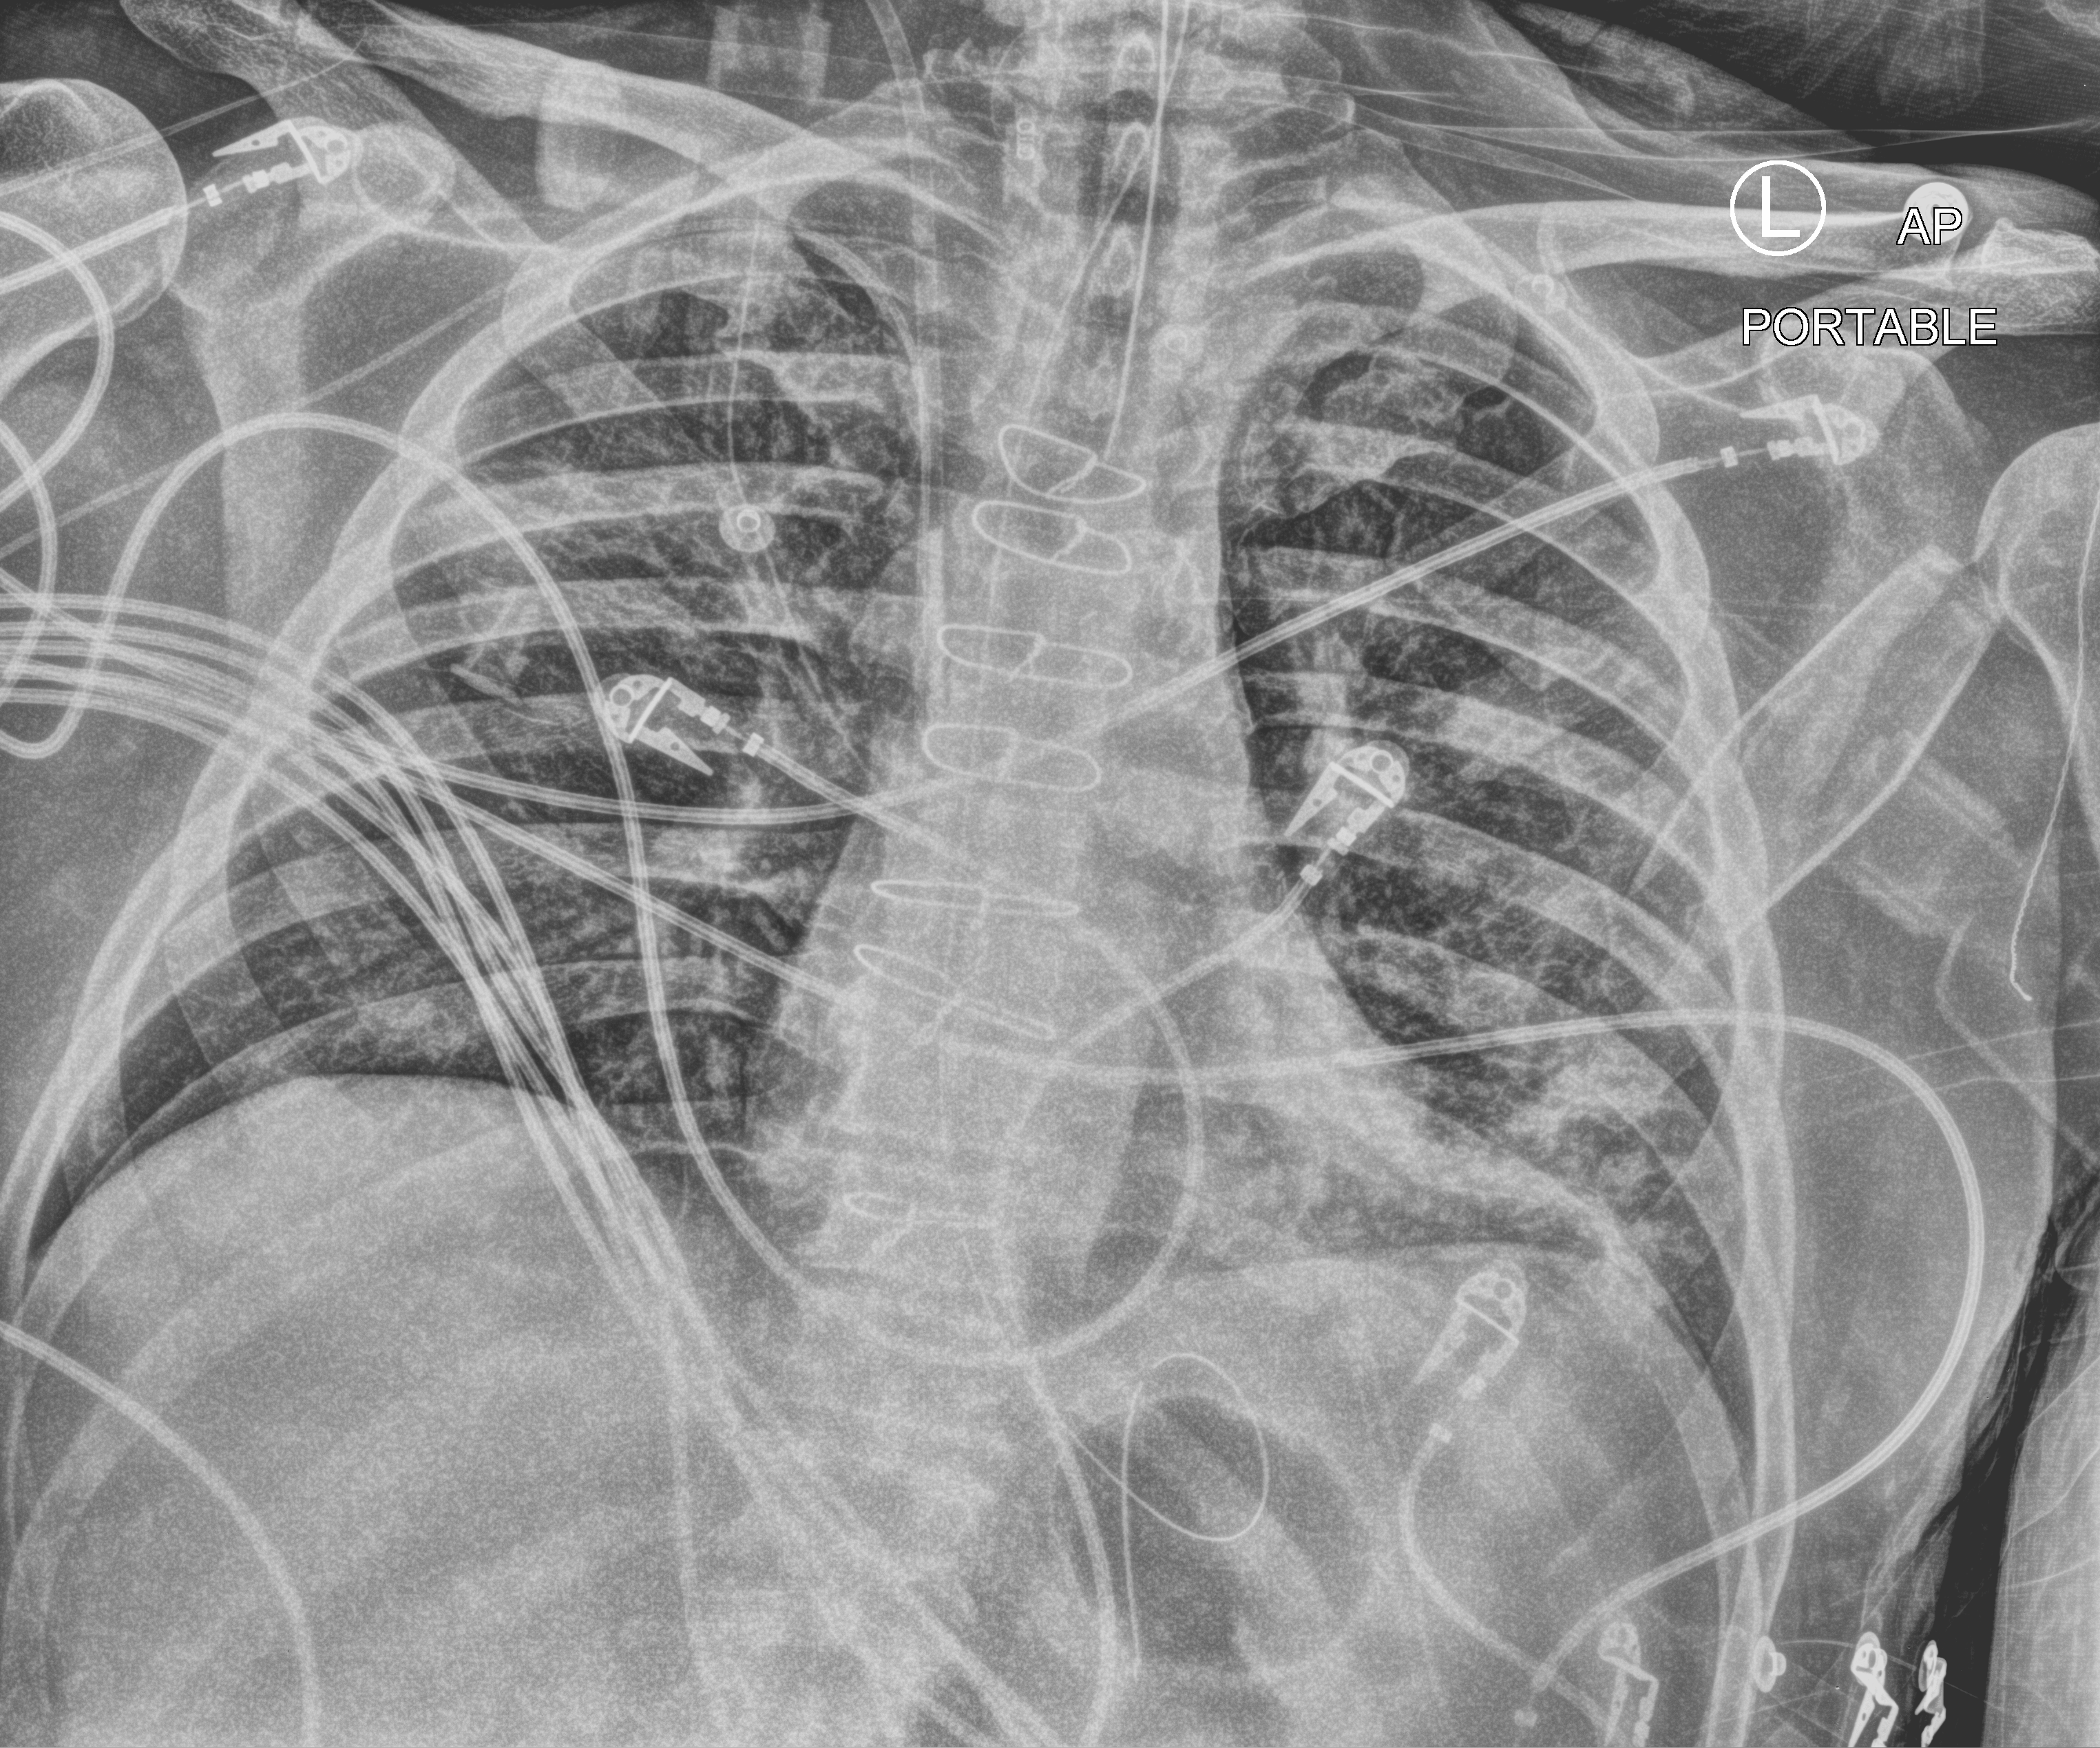
Bedside chest radiograph (computed radiography); anteroposterior (AP) projection. Male patient hospitalised with COVID-19, age 60–74 years.
Hospital-stay facts (about this admission, not read from this image; timing relative to this image not recorded): hypertension (admission record): yes.